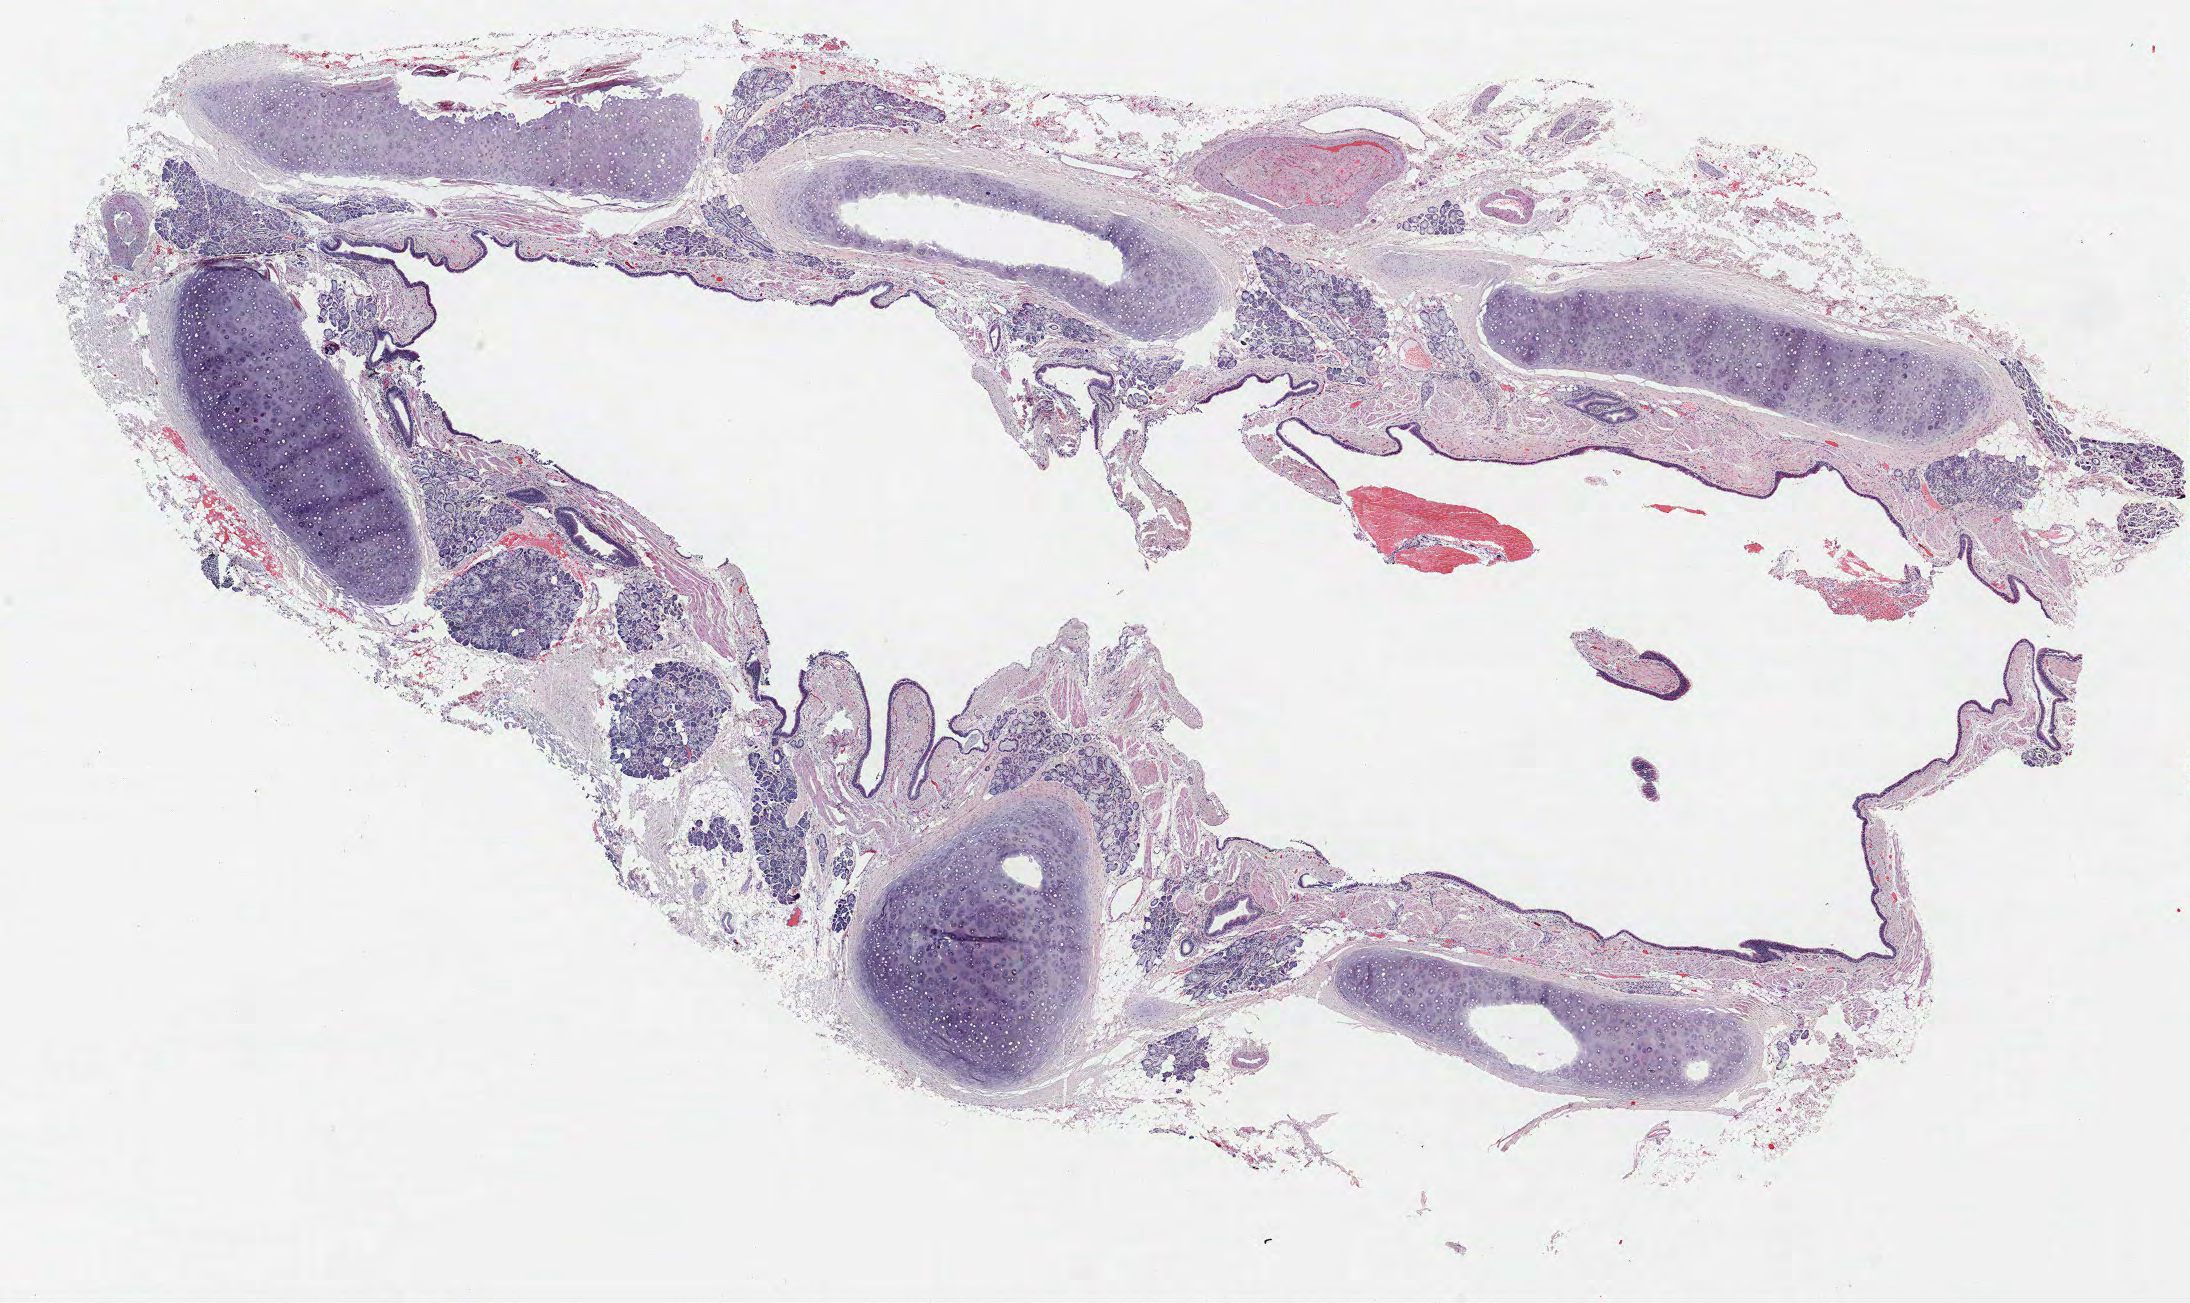
H&E-stained whole-slide image — a low-resolution overview of the entire scanned area, about 17.5 x 10.4 mm; formalin-fixed paraffin-embedded (FFPE) section; lung. Male patient, aged 63 at enrolment. Former smoker at enrolment. Grade: undifferentiated (G4).
* participant's lung-cancer diagnosis: Large cell carcinoma, NOS (ICD-O-3 8012/3)
* tumour size (pathology): 45 mm
* primary tumour location (clinical record): right upper lobe
* stage (AJCC 6th edition): IB